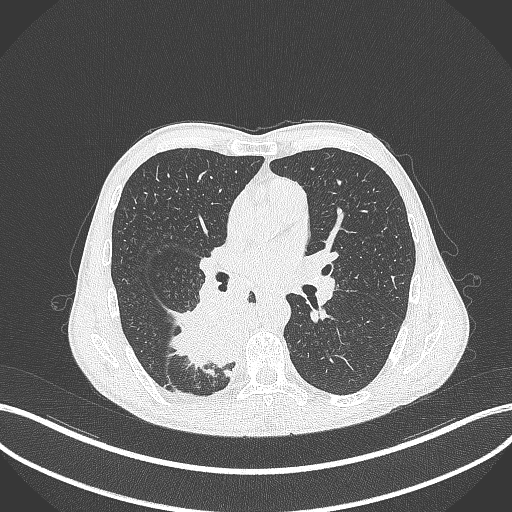
Chest CT, one axial slice. Slice 200 of 371 in the series (ordered by position). Lung window (W 1500 / L -600 HU). 512 × 512 image matrix, field of view 400 × 400 mm. Patient: male, 58 years. From the clinical record (not read from this slice): clinical TNM (as recorded): T3 N1 M1.
Outlined on this slice (bounding box drawn by a radiologist):
- lung tumour (recorded histology: squamous cell carcinoma): bounding box <164,283,251,376> (left, top, right, bottom; pixels)